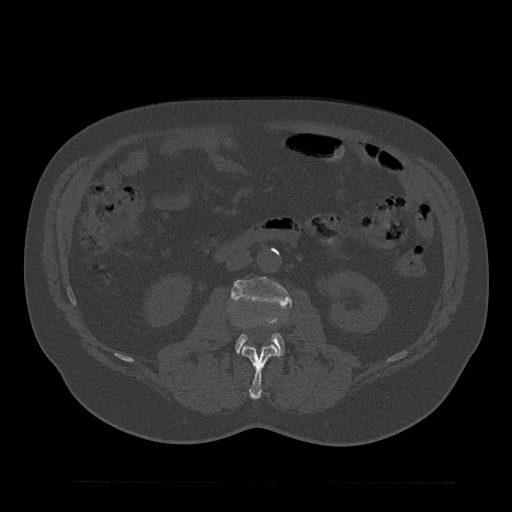
CT including the spine, one axial slice; position 68 of 797 along the scan axis; bone window (W 1800 / L 400 HU); 0.5 mm slice thickness; 512 × 512 image matrix. Patient: male, 61 years. From the clinical record (not read from this slice): primary cancer: prostate.
Structures marked on this image (semi-automatically segmented with operator editing):
- L2 vertebra: bounding box <241,345,279,399> (left, top, right, bottom; pixels)
- L3 vertebra: <232,277,292,356>